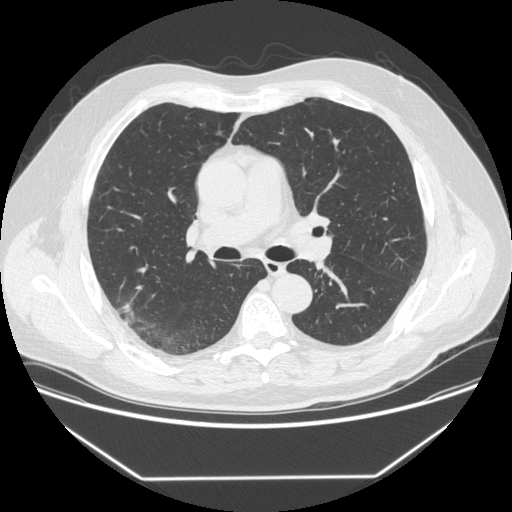
Low-dose screening chest CT, axial slice, baseline annual screen, lung window (W 1500 / L -600 HU), 120 kVp, slice 216 of 342 in the series, 512 × 512 image matrix. Male, age 64 years at enrolment. Former smoker at enrolment.
Lesion marked by an expert reader, bounding box [x1, y1, x2, y2] px = [103, 299, 146, 334]. The exam's reader record, not a measurement of the box and not confirmed to be the same lesion: non-calcified nodule or mass ≥4 mm, right upper lobe, 12 × 12 mm, smooth margins, soft tissue attenuation. Participant outcome: lung cancer diagnosed 92 days after this screen — adenocarcinoma, NOS, right upper lobe, poorly differentiated (G3), stage IIIB (AJCC 6th edition), 15 mm at pathology.